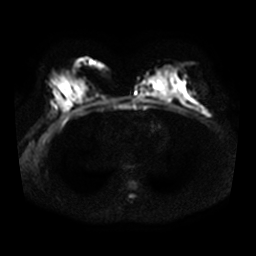
Breast MRI, one axial slice. Position 18 of 34 along the scan axis. Diffusion-weighted series; image 2 of 4 stored at this slice position (different b-values; order by instance number). 3 T. 5 mm slice thickness. 256 × 256 image matrix, field of view 340 × 340 mm. Female patient.
Annotated regions visible in this slice (outlined manually by an expert reader):
- tumour on diffusion-weighted imaging: bounding box <205,113,209,116> (left, top, right, bottom; pixels)